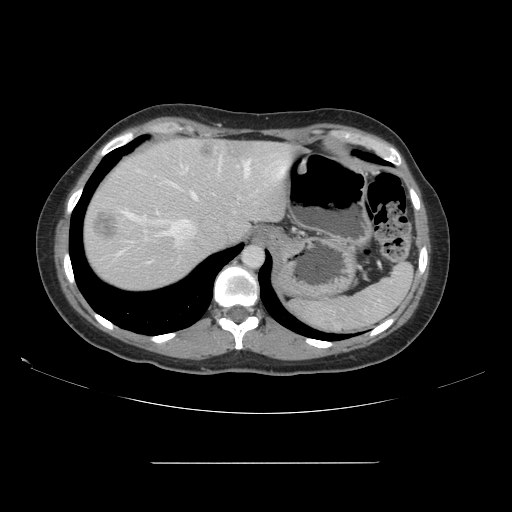
Contrast-enhanced abdominal CT, one axial slice; slice 124 of 151 in the series (ordered by position); intravenous contrast given; soft-tissue window (W 400 / L 40 HU); 512 × 512 image matrix, field of view 421 × 421 mm. Female patient, age 46 years. From the clinical record (not read from this slice): diagnosis: colorectal cancer liver metastases, imaged before liver resection; multiple liver metastases: yes; largest metastasis: 3 cm; chemotherapy before resection: no.
Structures marked on this image (manually delineated by an expert):
- hepatic veins: bounding box (x1, y1, x2, y2) in pixels: (121, 157, 253, 245)
- liver: (83, 139, 299, 291)
- planned liver remnant (the part of the liver to remain after resection): (95, 140, 299, 245)
- liver metastasis: (93, 214, 118, 240)
- liver metastasis: (200, 144, 214, 158)